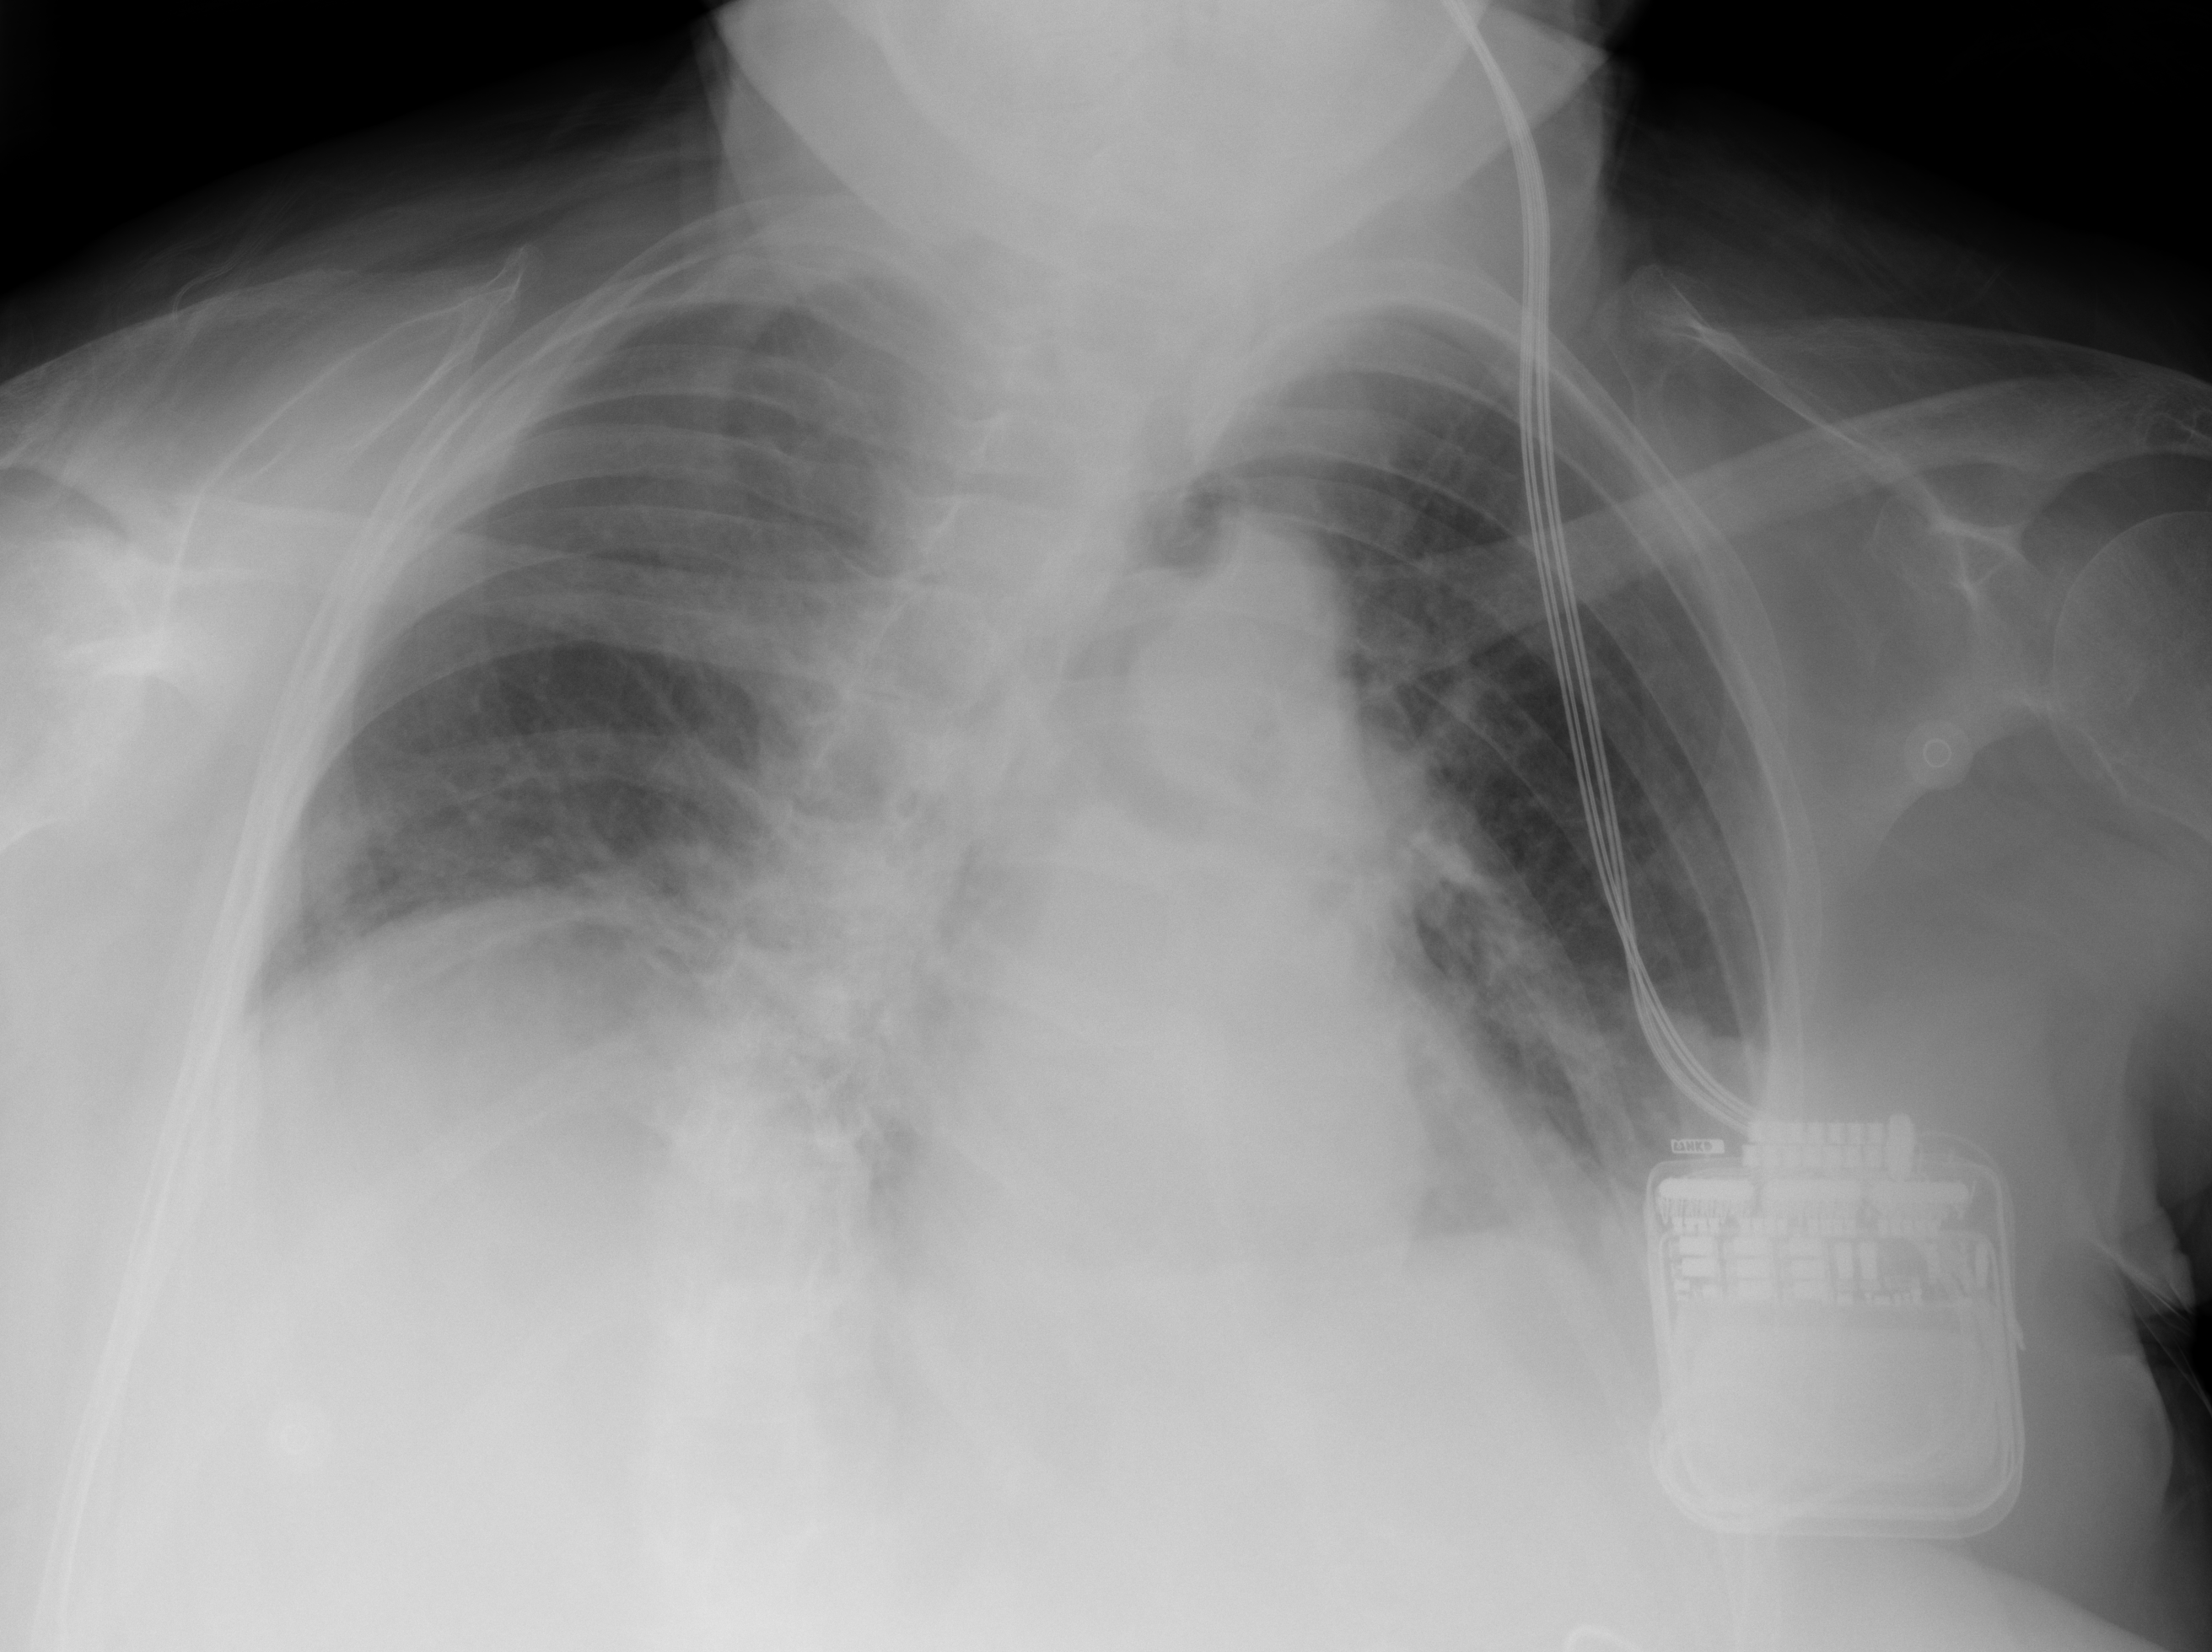
Chest X-ray (portable), AP projection. Female patient, age 81 years; imaged 0 days after the COVID-19 diagnosis.
Radiologist's key findings for this exam: Bibasilar atelectasis and low lung volumes.